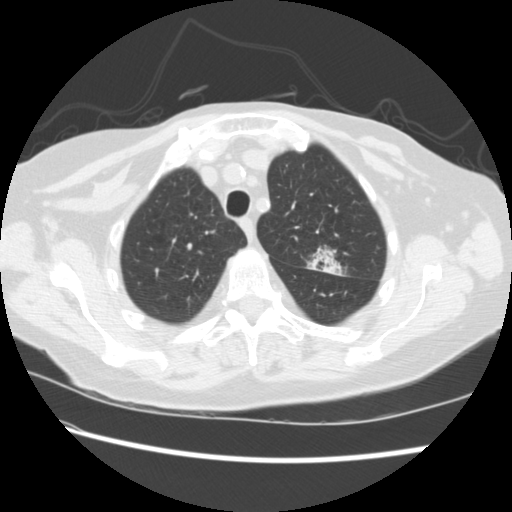
Low-dose screening chest CT, one axial slice; position 176 of 224 along the scan axis; lung window (W 1500 / L -600 HU); 512 × 512 image matrix, field of view 340 × 340 mm.
Structures marked on this image (expert manual segmentation):
- lesion 1 (tumor, upper lobe of left lung): box from (x=307, y=248) to (x=343, y=276) px